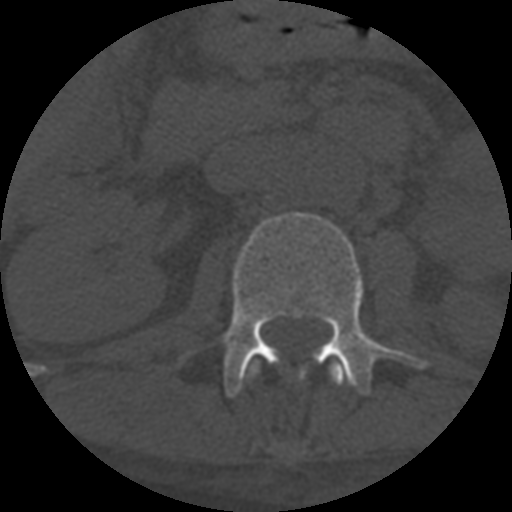
CT including the spine, one axial slice. Position 267 of 708 along the scan axis. 120 kVp. One of 3 acquisitions stored at this slice position. Bone window (W 1800 / L 400 HU). 1.25 mm slice thickness. 512 × 512 image matrix, field of view 160 × 160 mm. Patient age 55 years. From the clinical record (not read from this slice): primary cancer: colon.
Outlined on this slice (semi-automatic segmentation, software-assisted and operator-edited):
- L1 vertebra: bounding box [x1, y1, x2, y2] px = [243, 362, 348, 386]
- L2 vertebra: [176, 212, 426, 398]